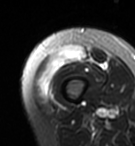
MRI of an extremity soft-tissue mass, one axial slice; position 10 of 95 along the scan axis; T2-weighted fat-saturated; MR volume resampled by the dataset authors to the PET/CT grid (not the native acquisition matrix); 3.27 mm slice thickness; 135 × 146 image matrix. Female patient. Case-level facts recorded for this patient, not image findings: histological type: pleiomorphic undifferentiated sarcoma; grade: high; site of the primary tumour: right quadricep.
Annotated regions visible in this slice (expert contour drawn on MRI and transferred to this co-registered scan by the dataset authors):
- gross tumour volume including surrounding oedema: bounding box [x1, y1, x2, y2] px = [35, 45, 88, 96]